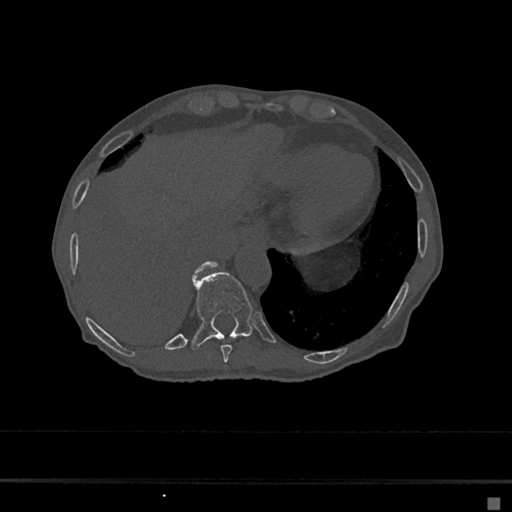
CT including the spine, one axial slice. Position 236 of 797 along the scan axis. Bone window (W 1800 / L 400 HU). 0.5 mm slice thickness. 512 × 512 image matrix. Female patient, age 68 years. Case-level facts recorded for this patient, not image findings: primary cancer: renal.
Annotated regions visible in this slice (semi-automatically segmented with operator editing):
- T10 vertebra: box from (x=192, y=272) to (x=256, y=349) px
- T11 vertebra: (x=194, y=261)–(x=217, y=277)
- T9 vertebra: (x=220, y=344)–(x=232, y=363)